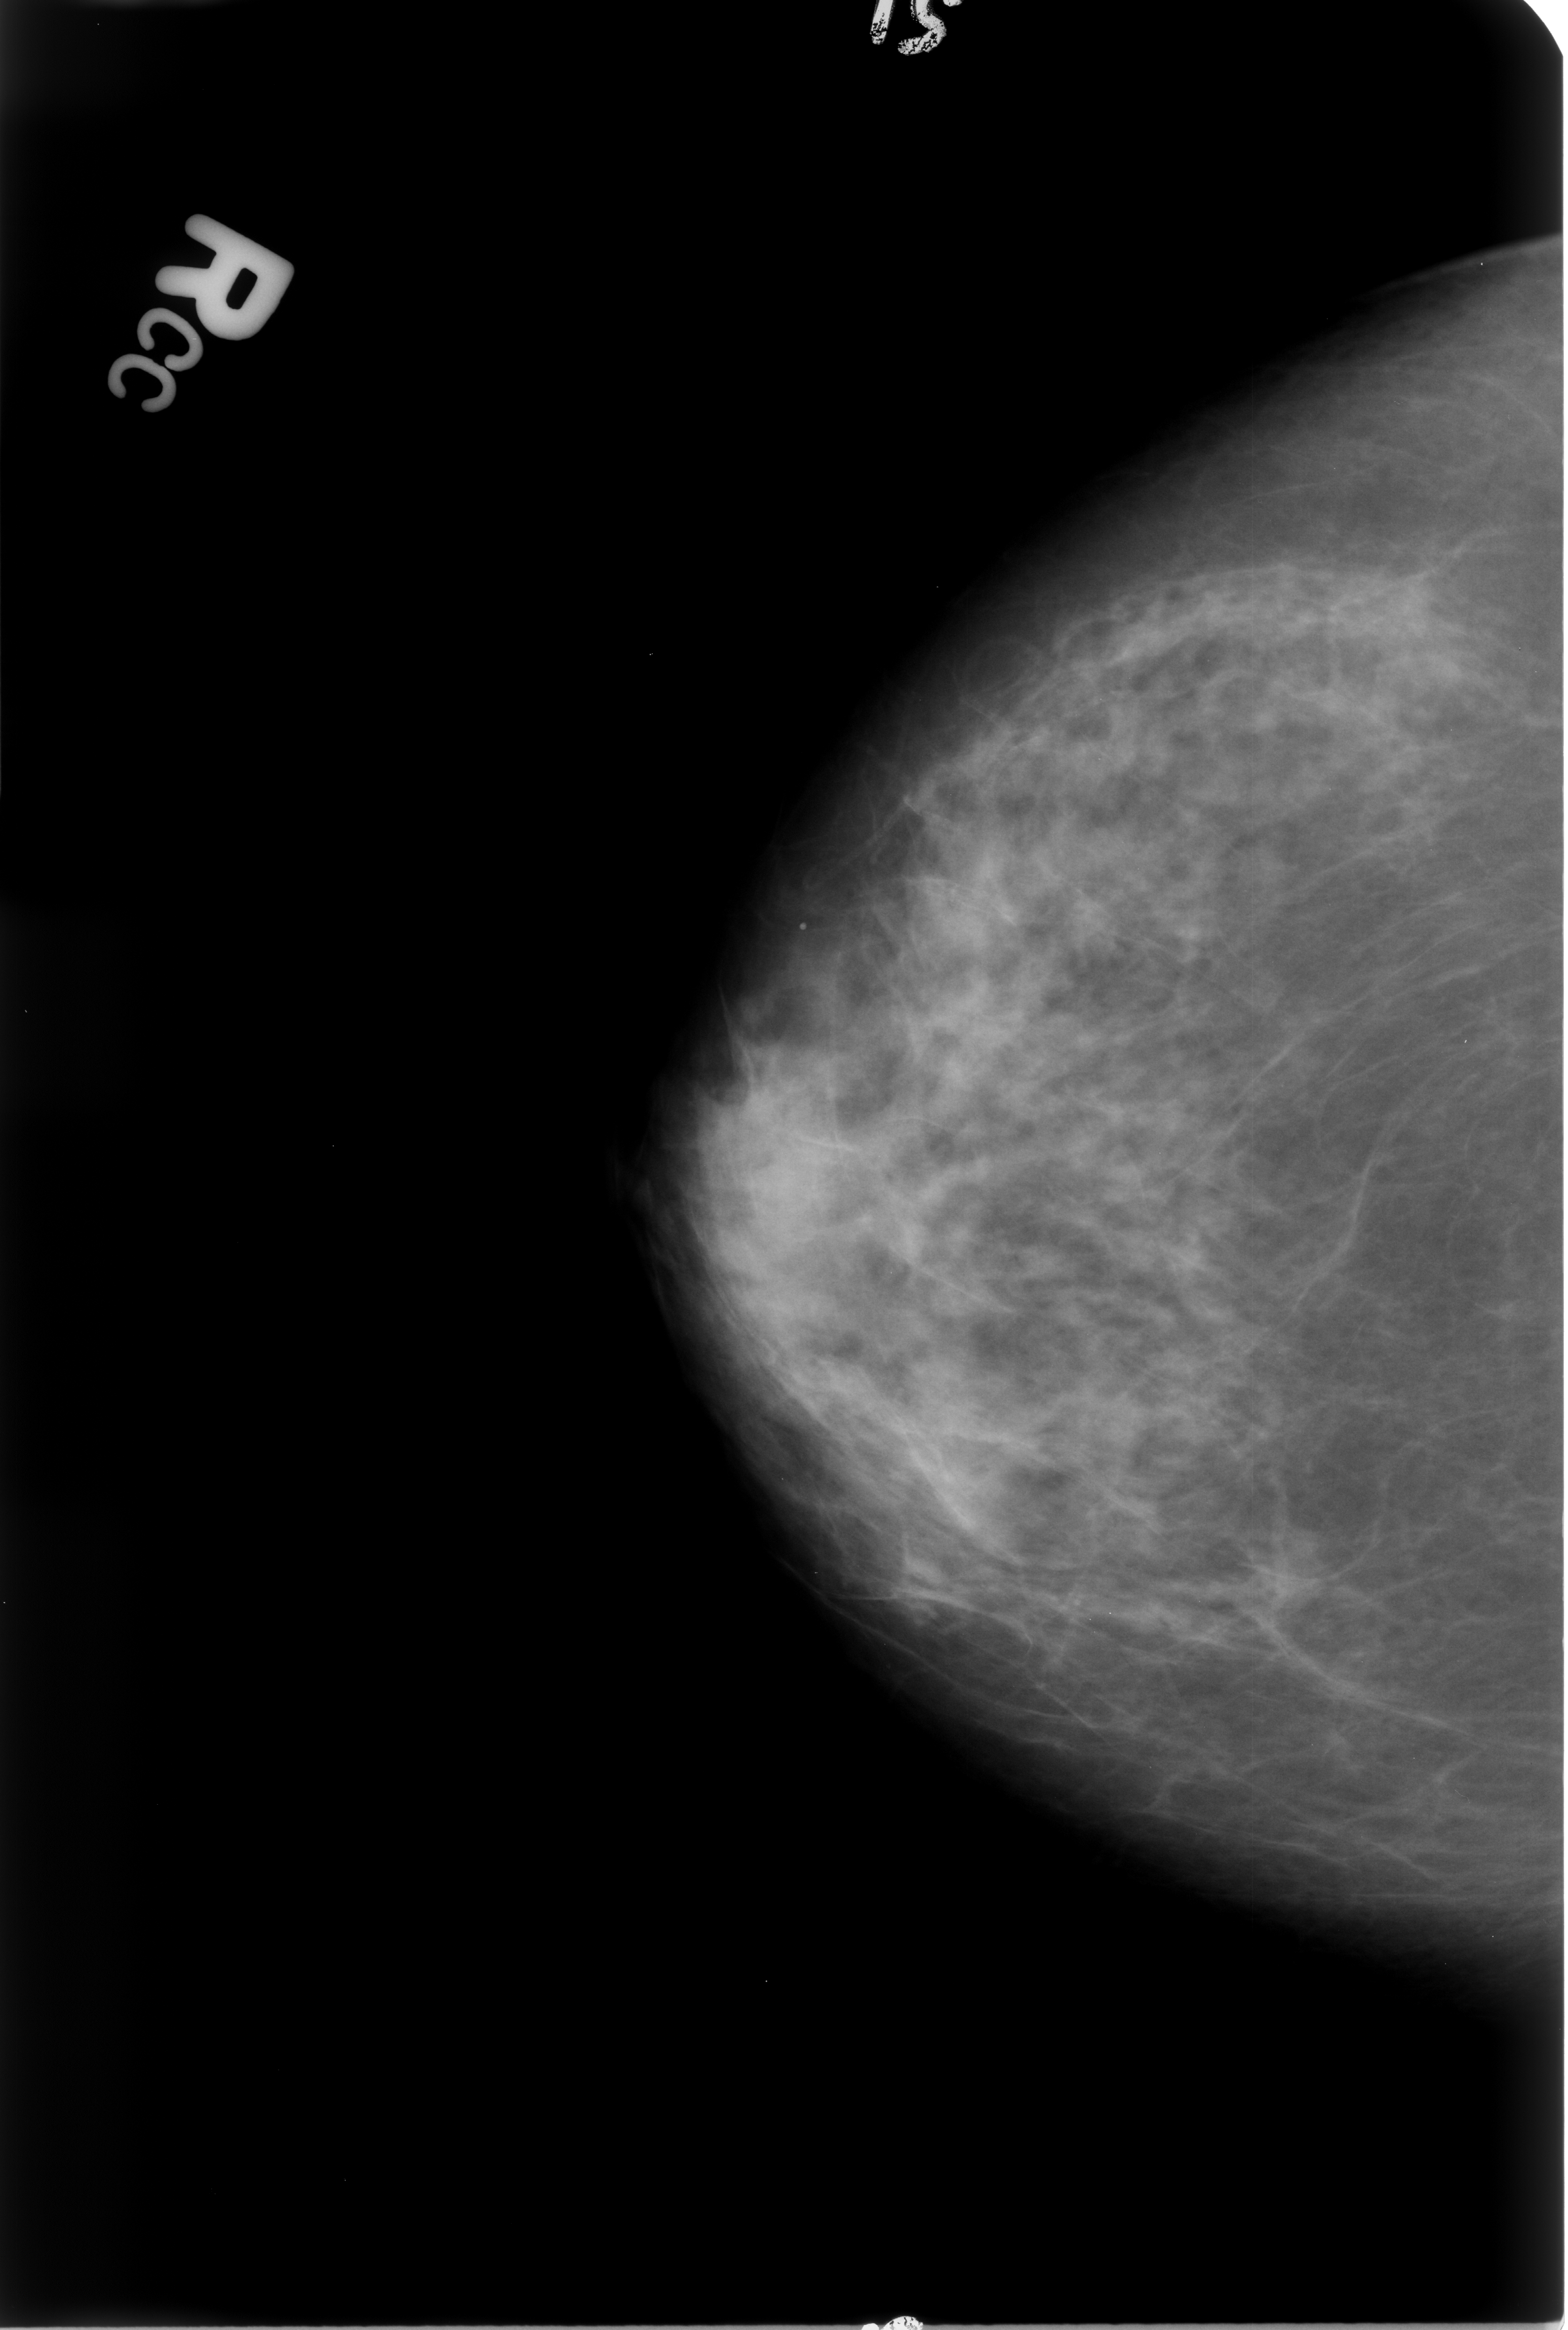
Scanned film-screen mammogram; right breast; CC view; breast composition: heterogeneously dense (BI-RADS density category 3 of 4); 1568 × 2330 image matrix.
Marked abnormalities (boxes around the expert regions of interest):
- Finding 1 of 2: calcifications, morphology punctate; BI-RADS assessment category 2; outcome (as recorded, no biopsy): benign without callback (not worked up further): bounding box (x1, y1, x2, y2) in pixels: (769, 883, 848, 961)
- Finding 2 of 2: calcifications, morphology vascular; BI-RADS assessment category 2; outcome (as recorded, no biopsy): benign without callback (not worked up further): (1025, 502, 1496, 824)